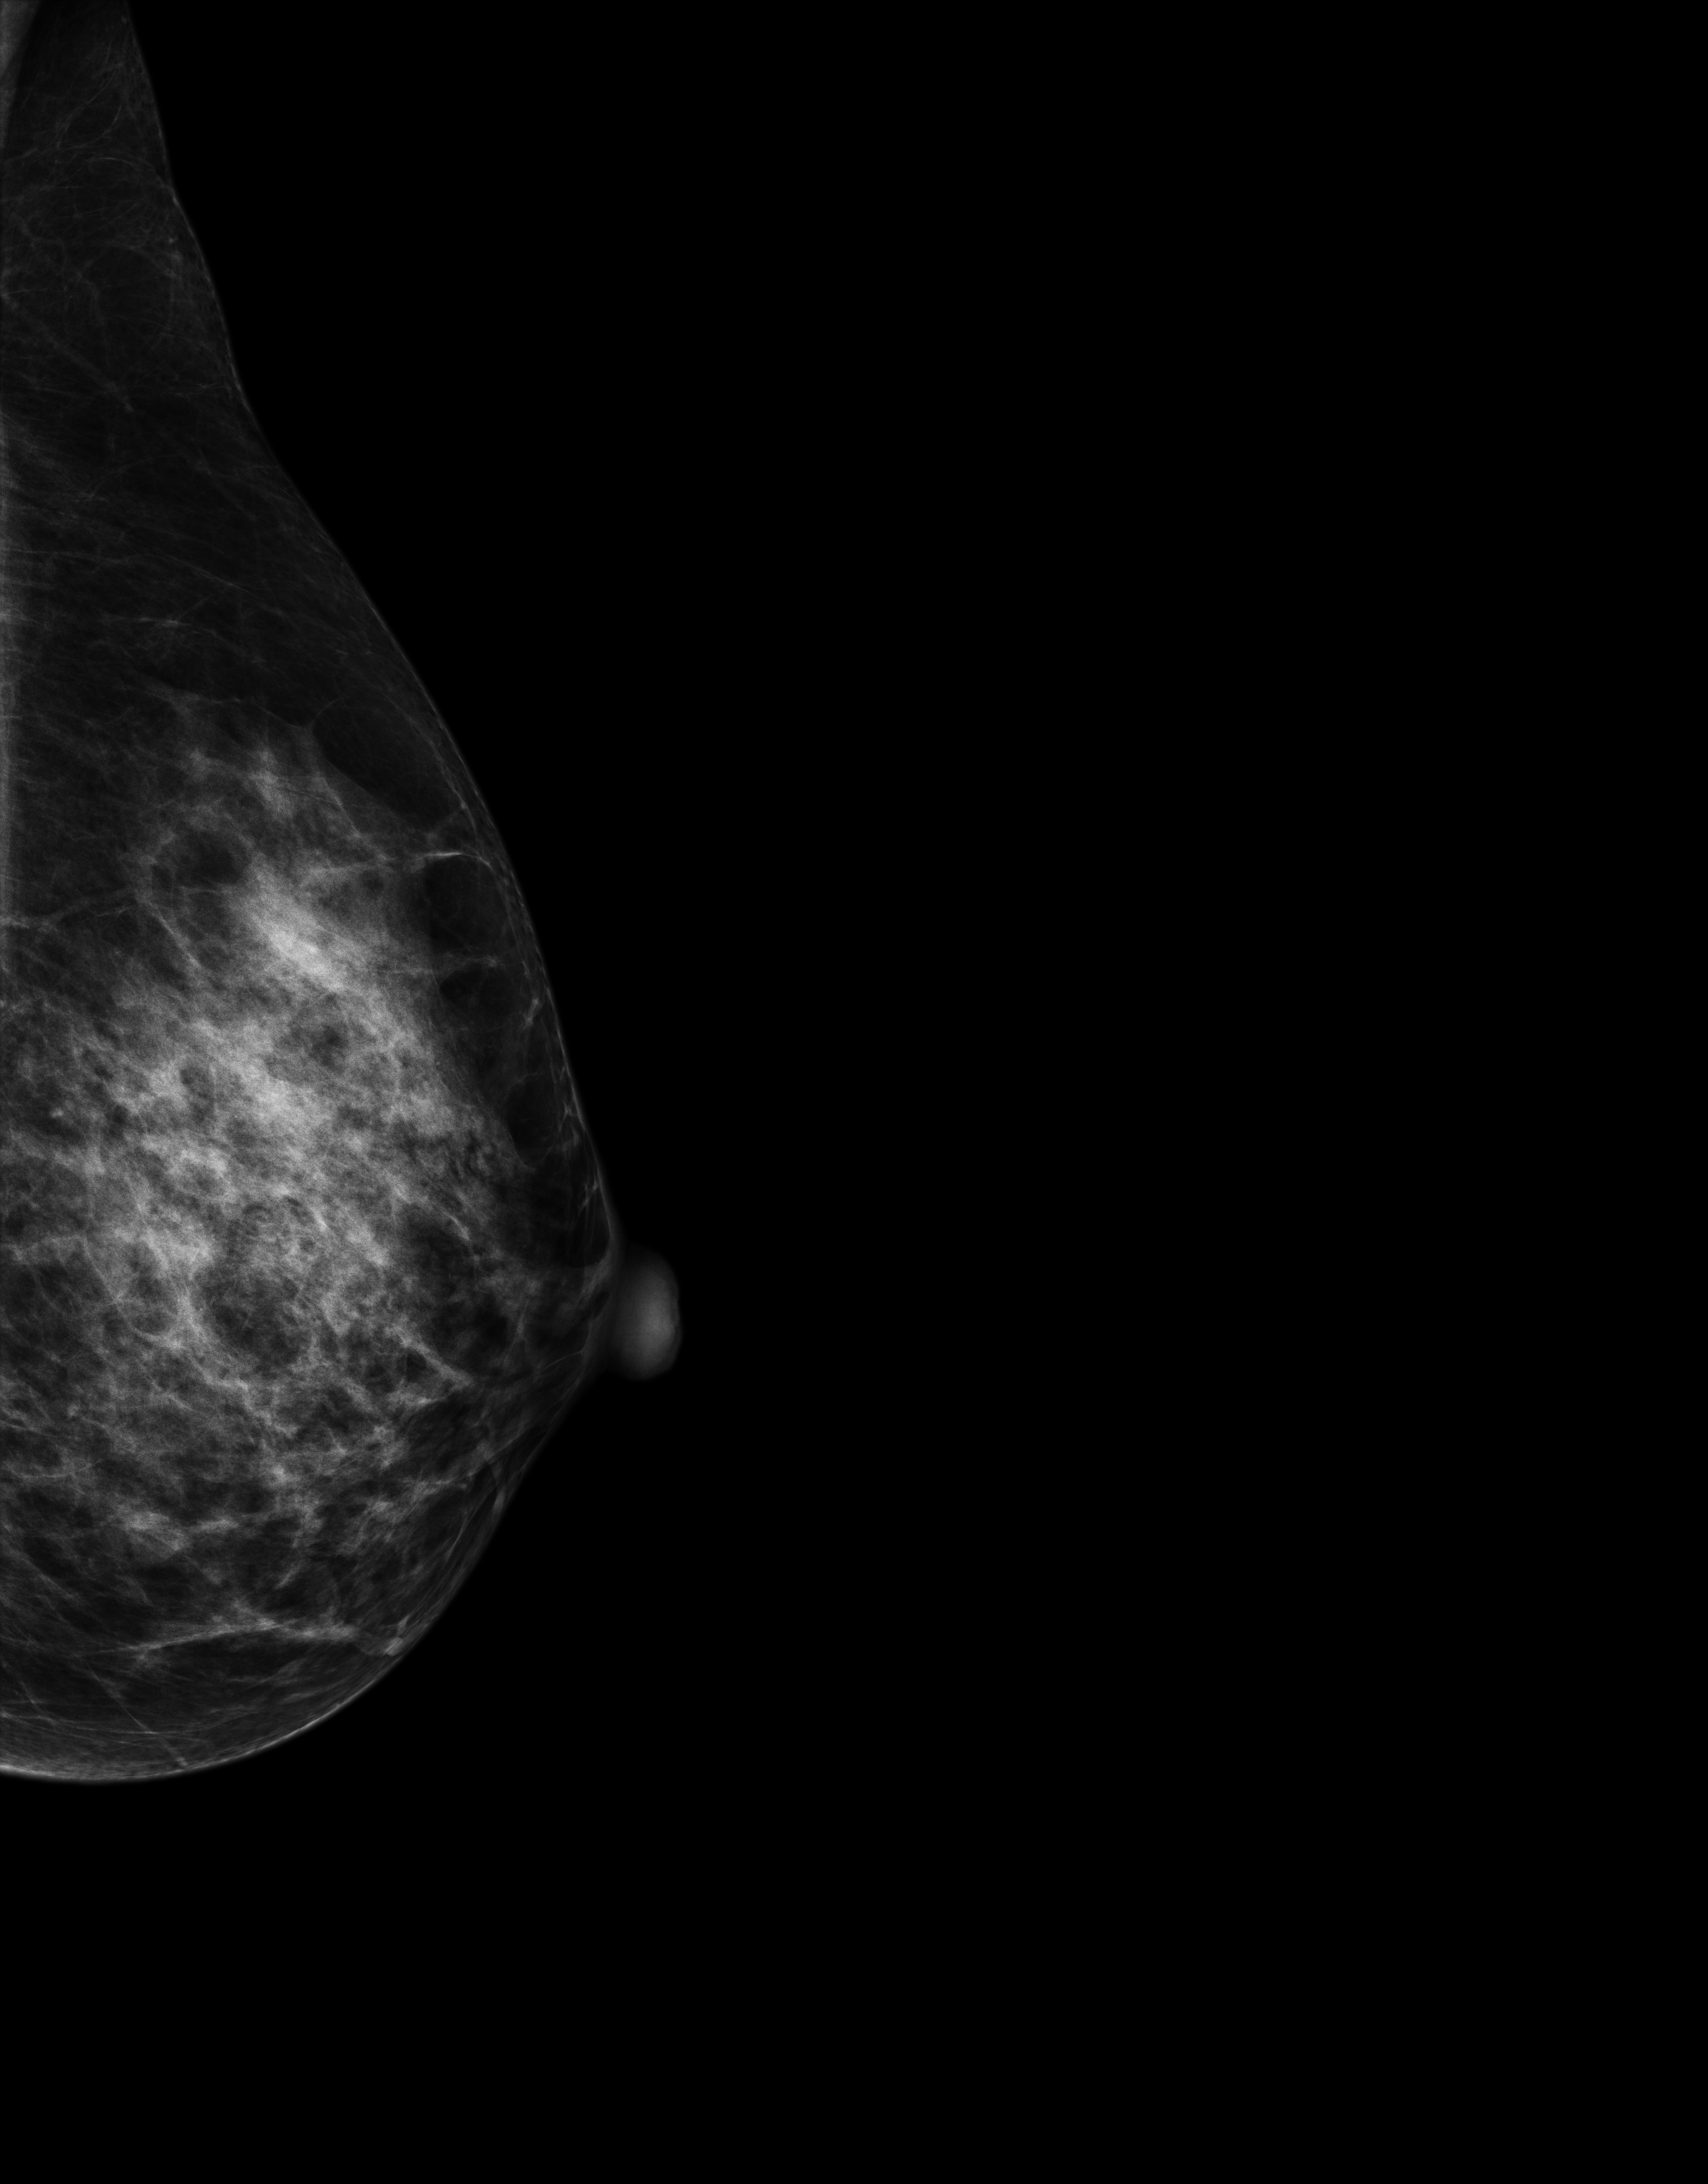
Screening examination; system: Senographe Essential ADS_56.21.3. Patient aged 42 years (female).
Image type: full-field digital mammogram. Breast: left. Projection: exaggerated CC view (lateral).